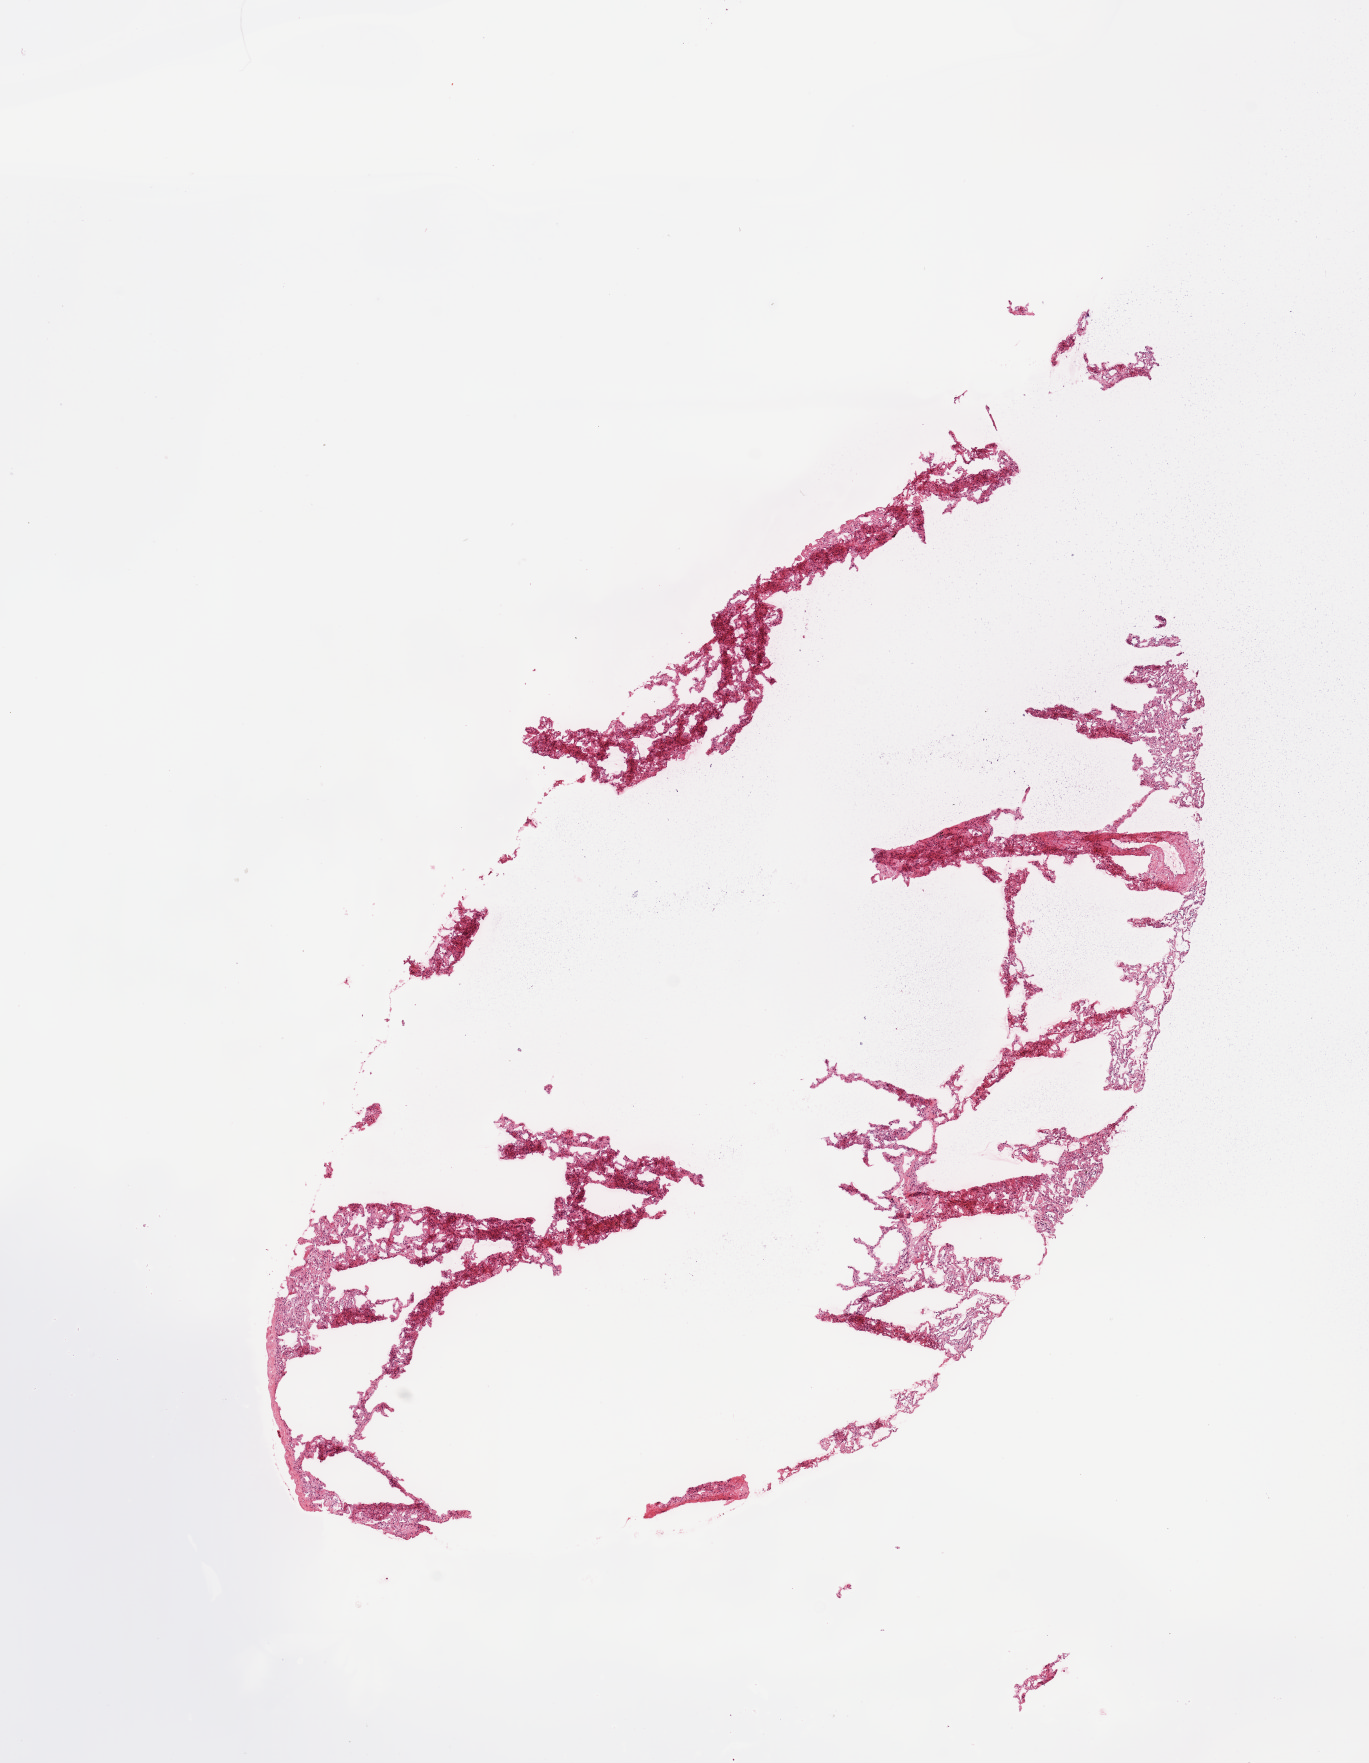
Whole-slide histology image, H&E-stained — low-resolution overview of the scanned area, about 10.8 x 13.9 mm (slide scanned at 20x), lung, normal (non-tumour) tissue. Female, 75 y/o.
This section: normal (non-tumour) tissue from the same patient. Patient diagnosis (cohort enrolment): squamous cell carcinoma (lung).